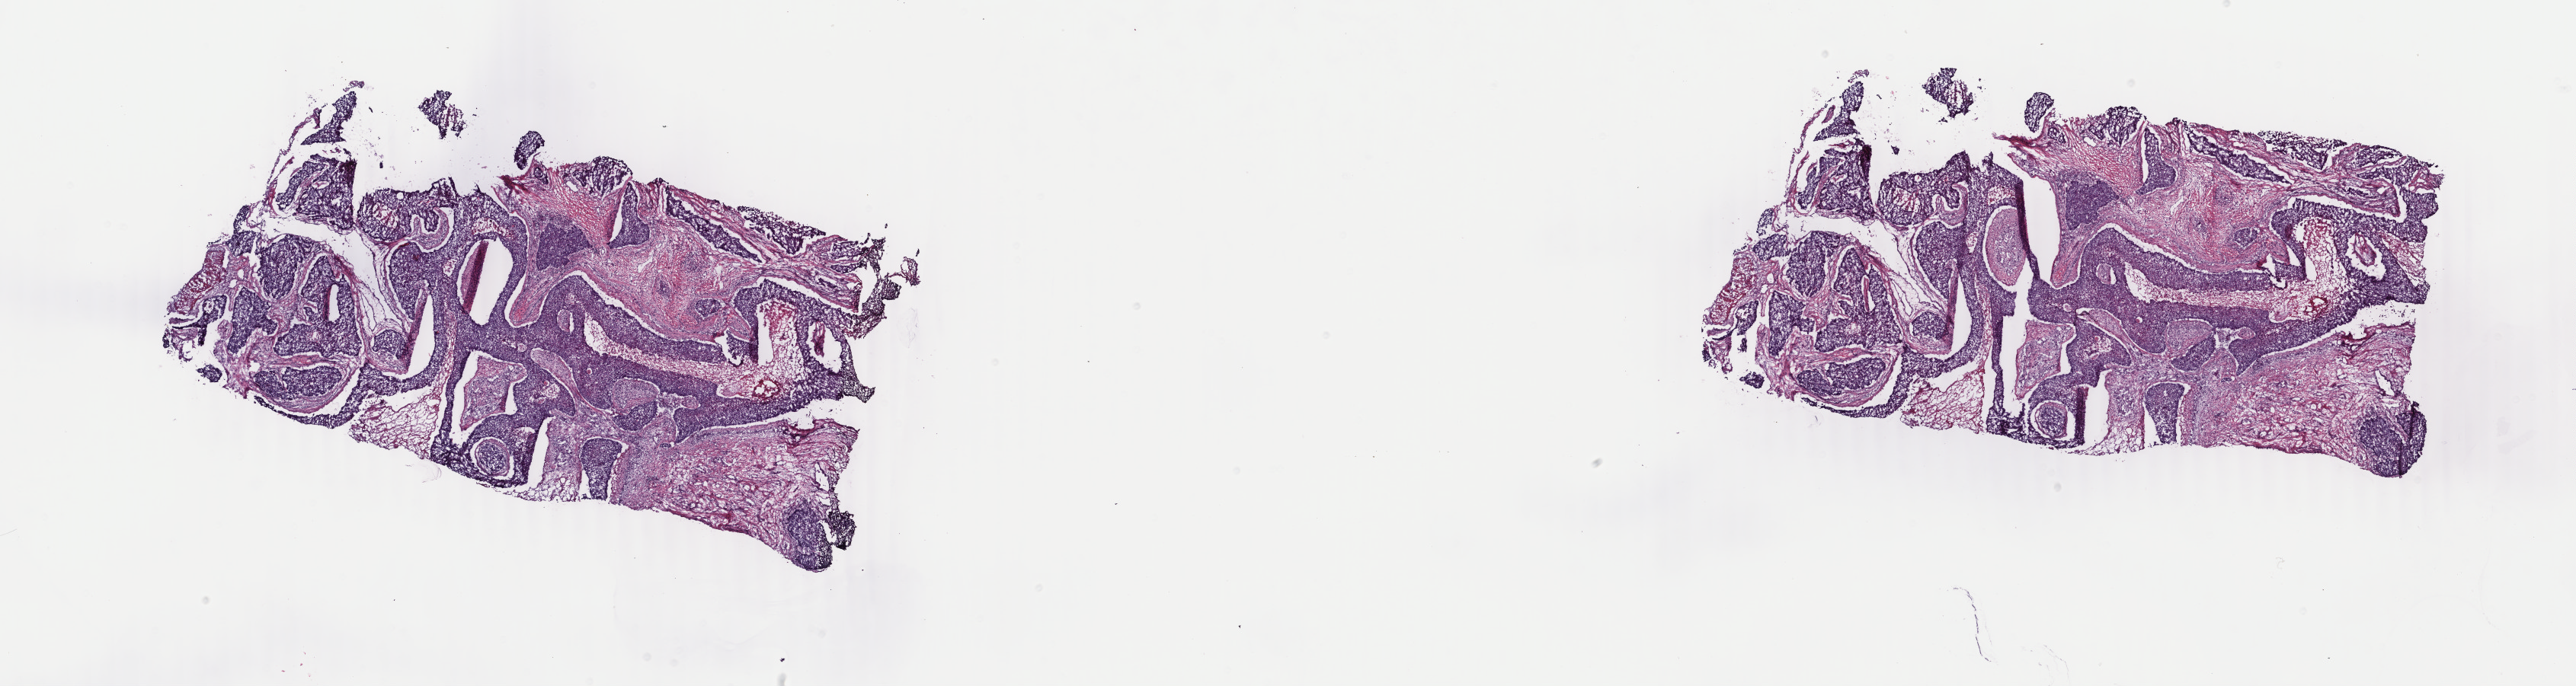
Digitized H&E tissue section (whole slide), whole scanned area (about 26.9 x 7.2 mm, acquisition: 40x scan) shown as a low-resolution overview; frozen section from the top of the tissue portion; primary tumour sample from the breast. Female patient; age at initial diagnosis 59 years. Slide review estimates, as recorded: tumour cells 80%, tumour nuclei 85%, normal cells 0%, stromal cells 18%, necrosis 2%. Infiltration values recorded for this section: lymphocyte infiltration 1%, monocyte infiltration 0%, neutrophil infiltration 0%.
AJCC pathologic stage: IV. Histologic diagnosis: Infiltrating duct carcinoma, NOS. TNM: T2 N2 M1.